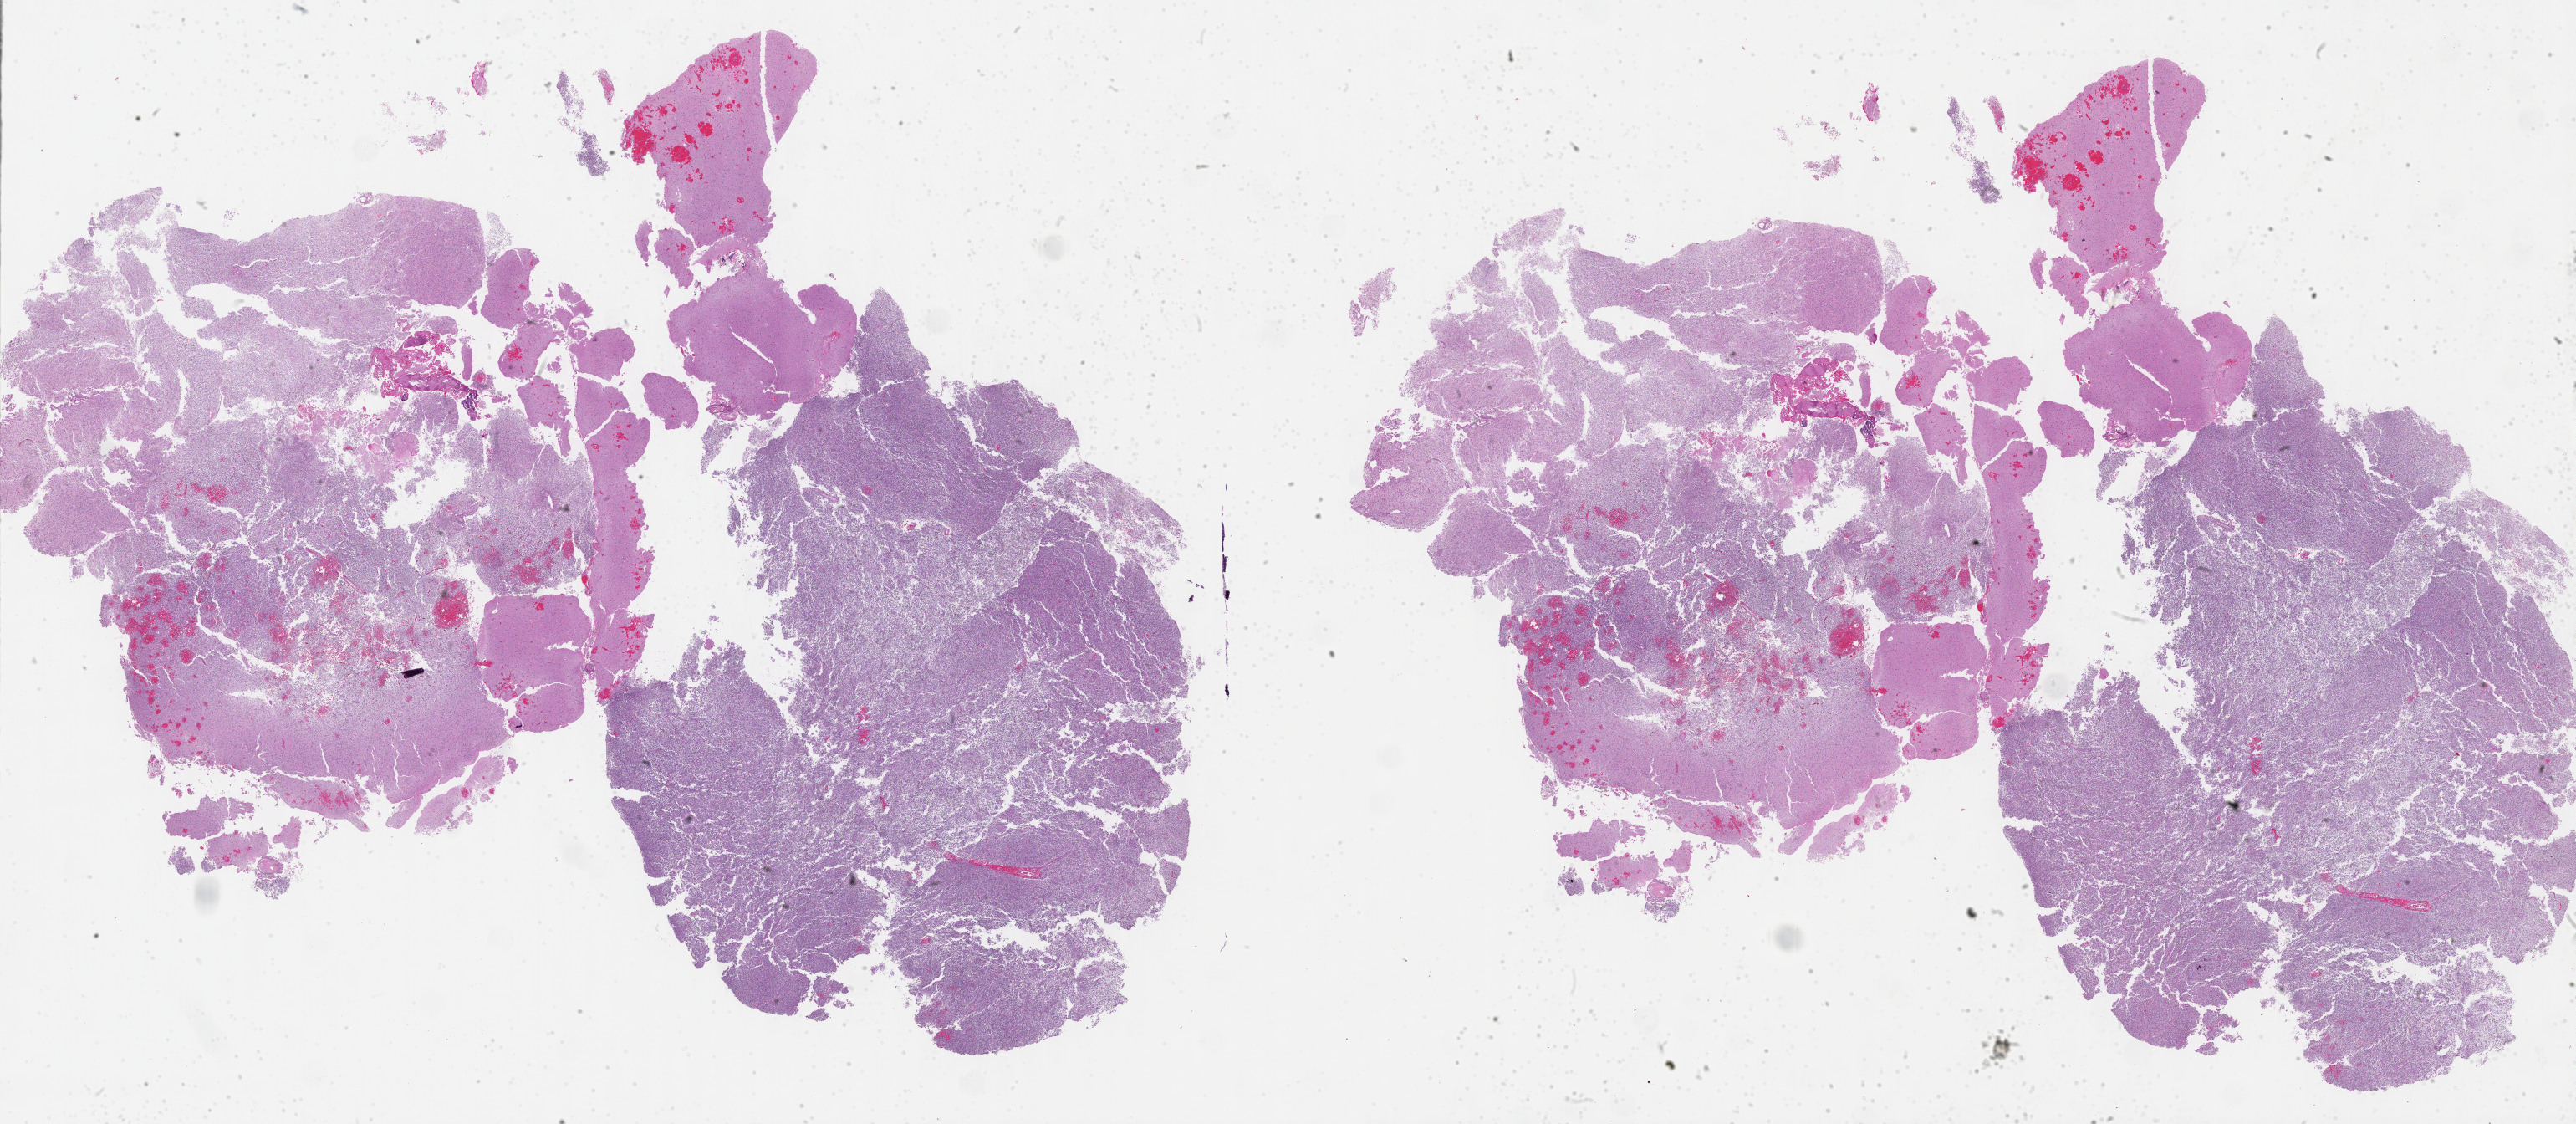
Whole-slide histology image, H&E-stained — whole scanned area (about 49.8 x 21.7 mm) shown as a low-resolution overview, FFPE section, brain, primary tumour sample. Female patient; age at initial diagnosis 37 years. Histologic grade: G3 (poorly differentiated).
* diagnosis: Astrocytoma, anaplastic (cerebrum)